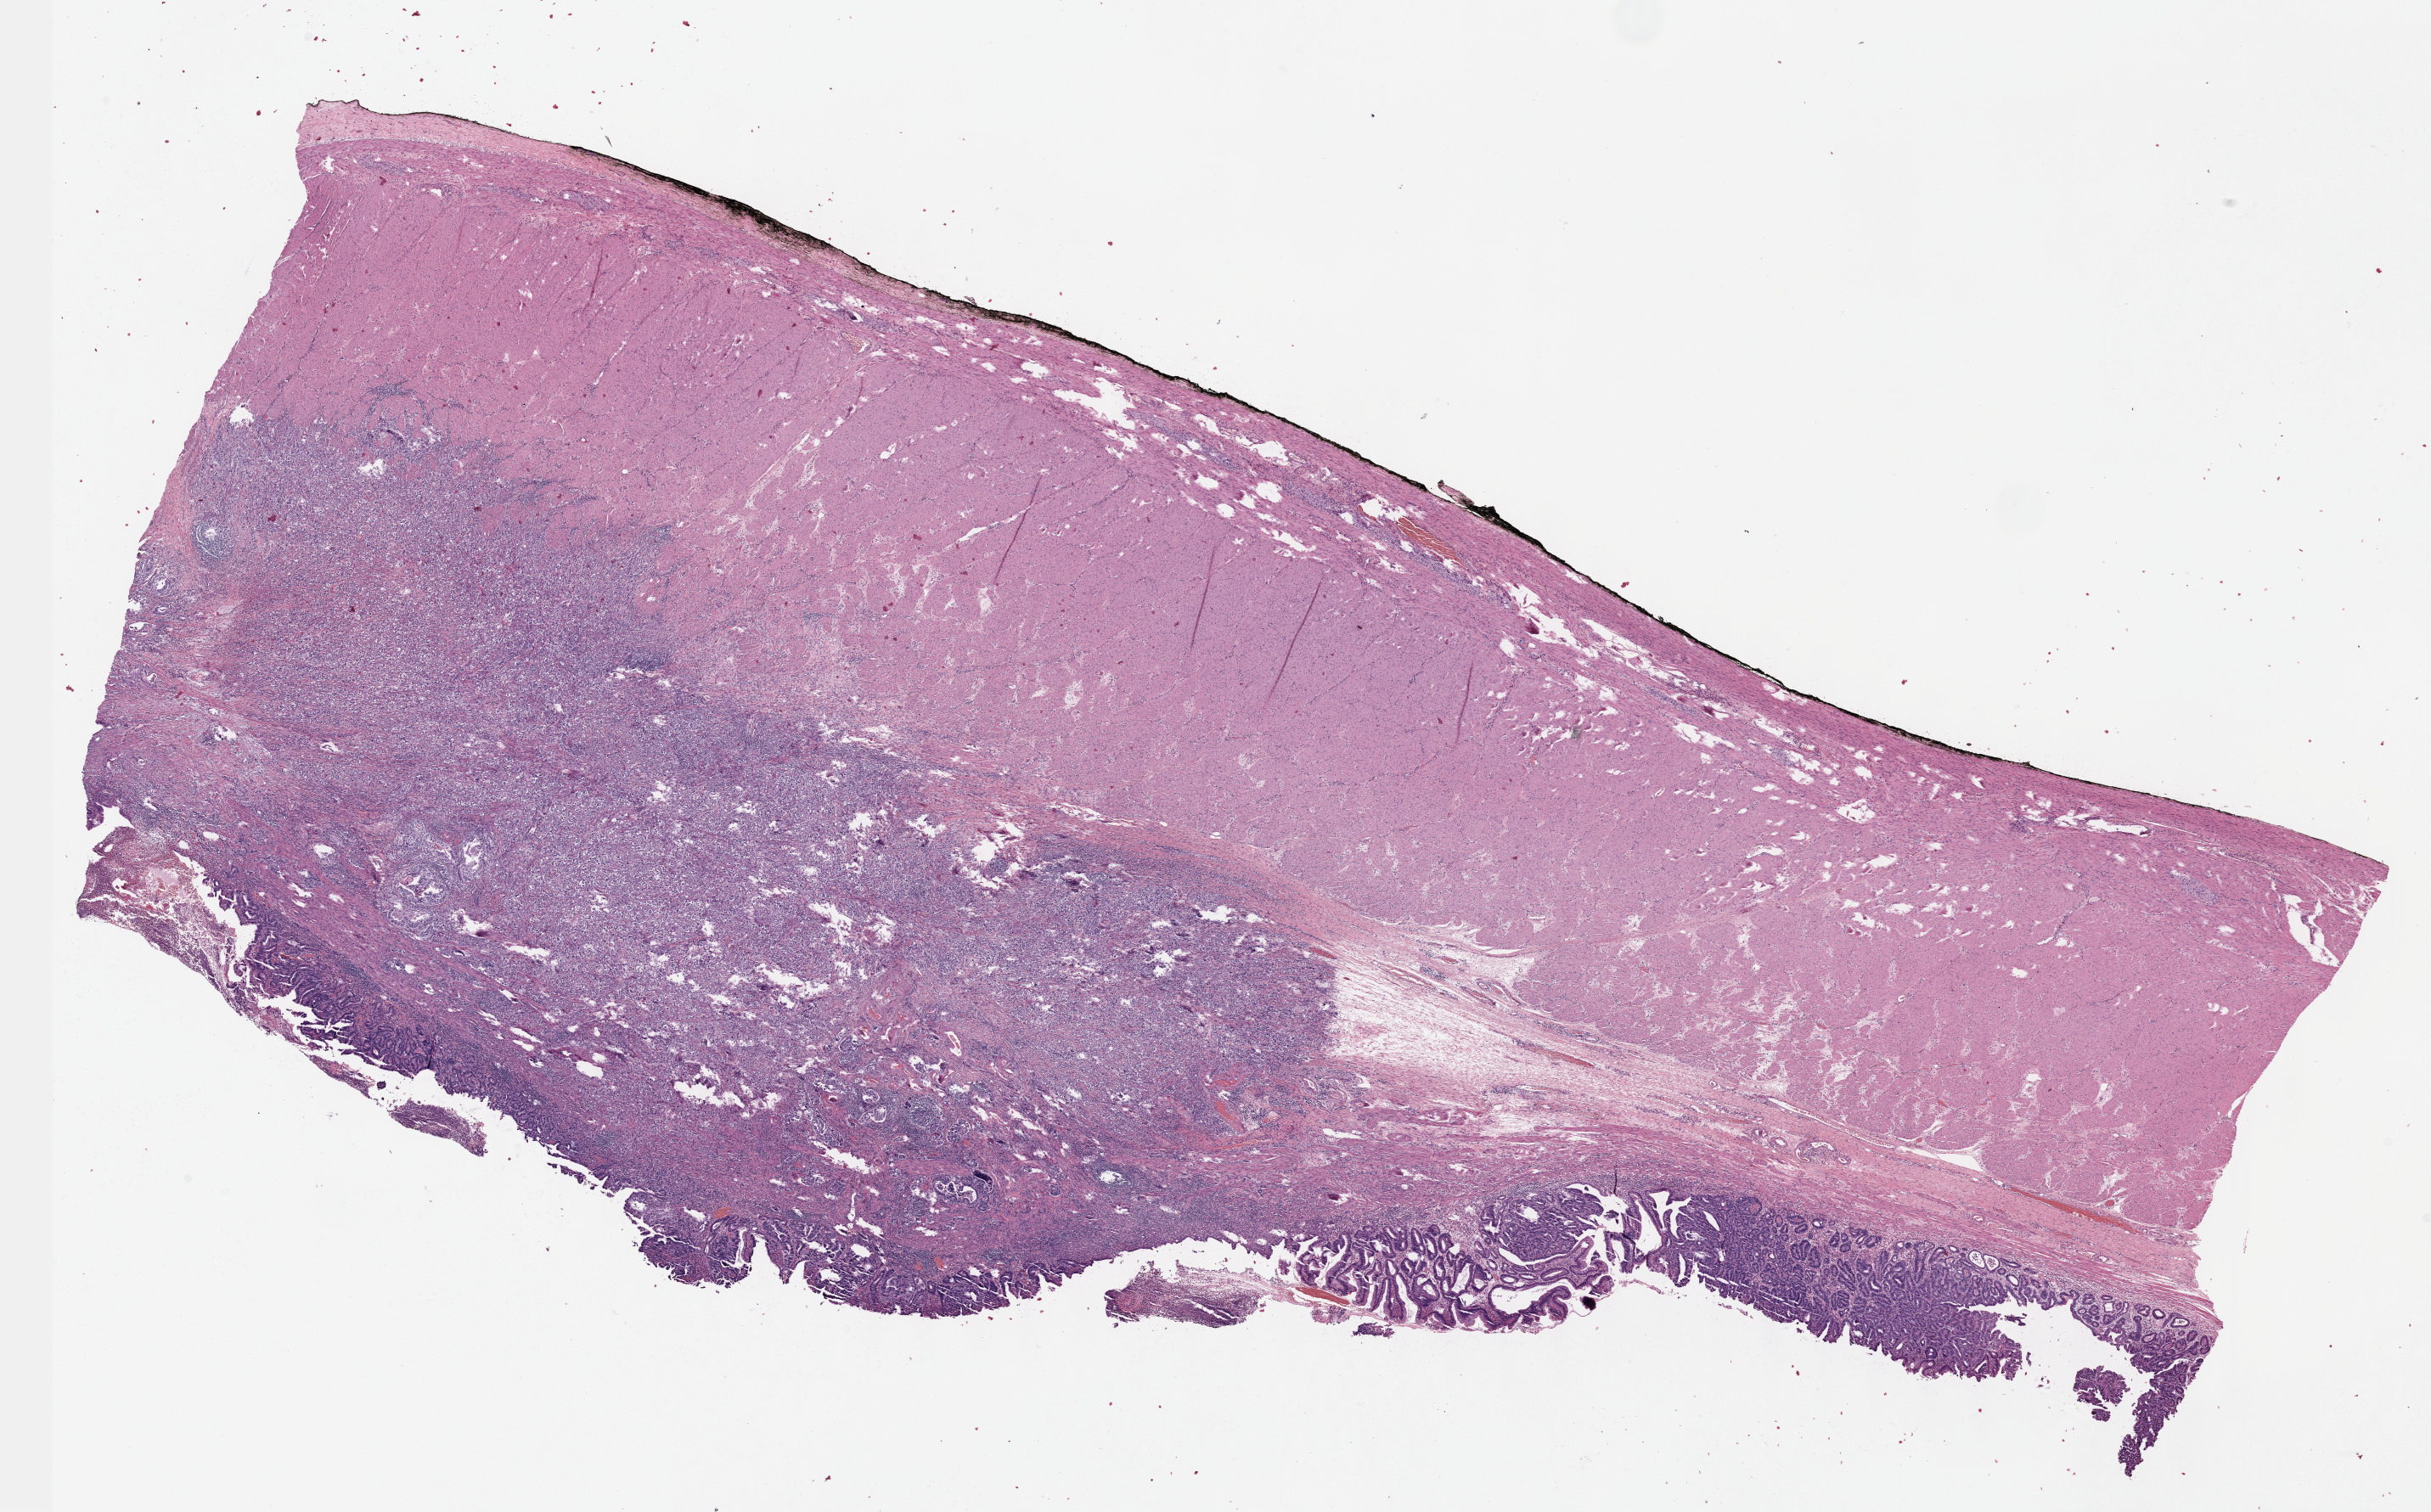
Hematoxylin and eosin (H&E) stained whole-slide image — whole scanned area (about 23.1 x 14.4 mm, from a 40x scan) shown as a low-resolution overview. Formalin-fixed paraffin-embedded (FFPE) diagnostic section. Stomach, primary tumour sample. Patient: male, age at initial diagnosis 74 years. Histologic grade: G3 (poorly differentiated).
TNM: T3 N2 M0. Histologic diagnosis: Adenocarcinoma, intestinal type (gastric antrum). AJCC pathologic stage: IIIB. Lymph nodes positive (case pathology): 14 of 34 examined.